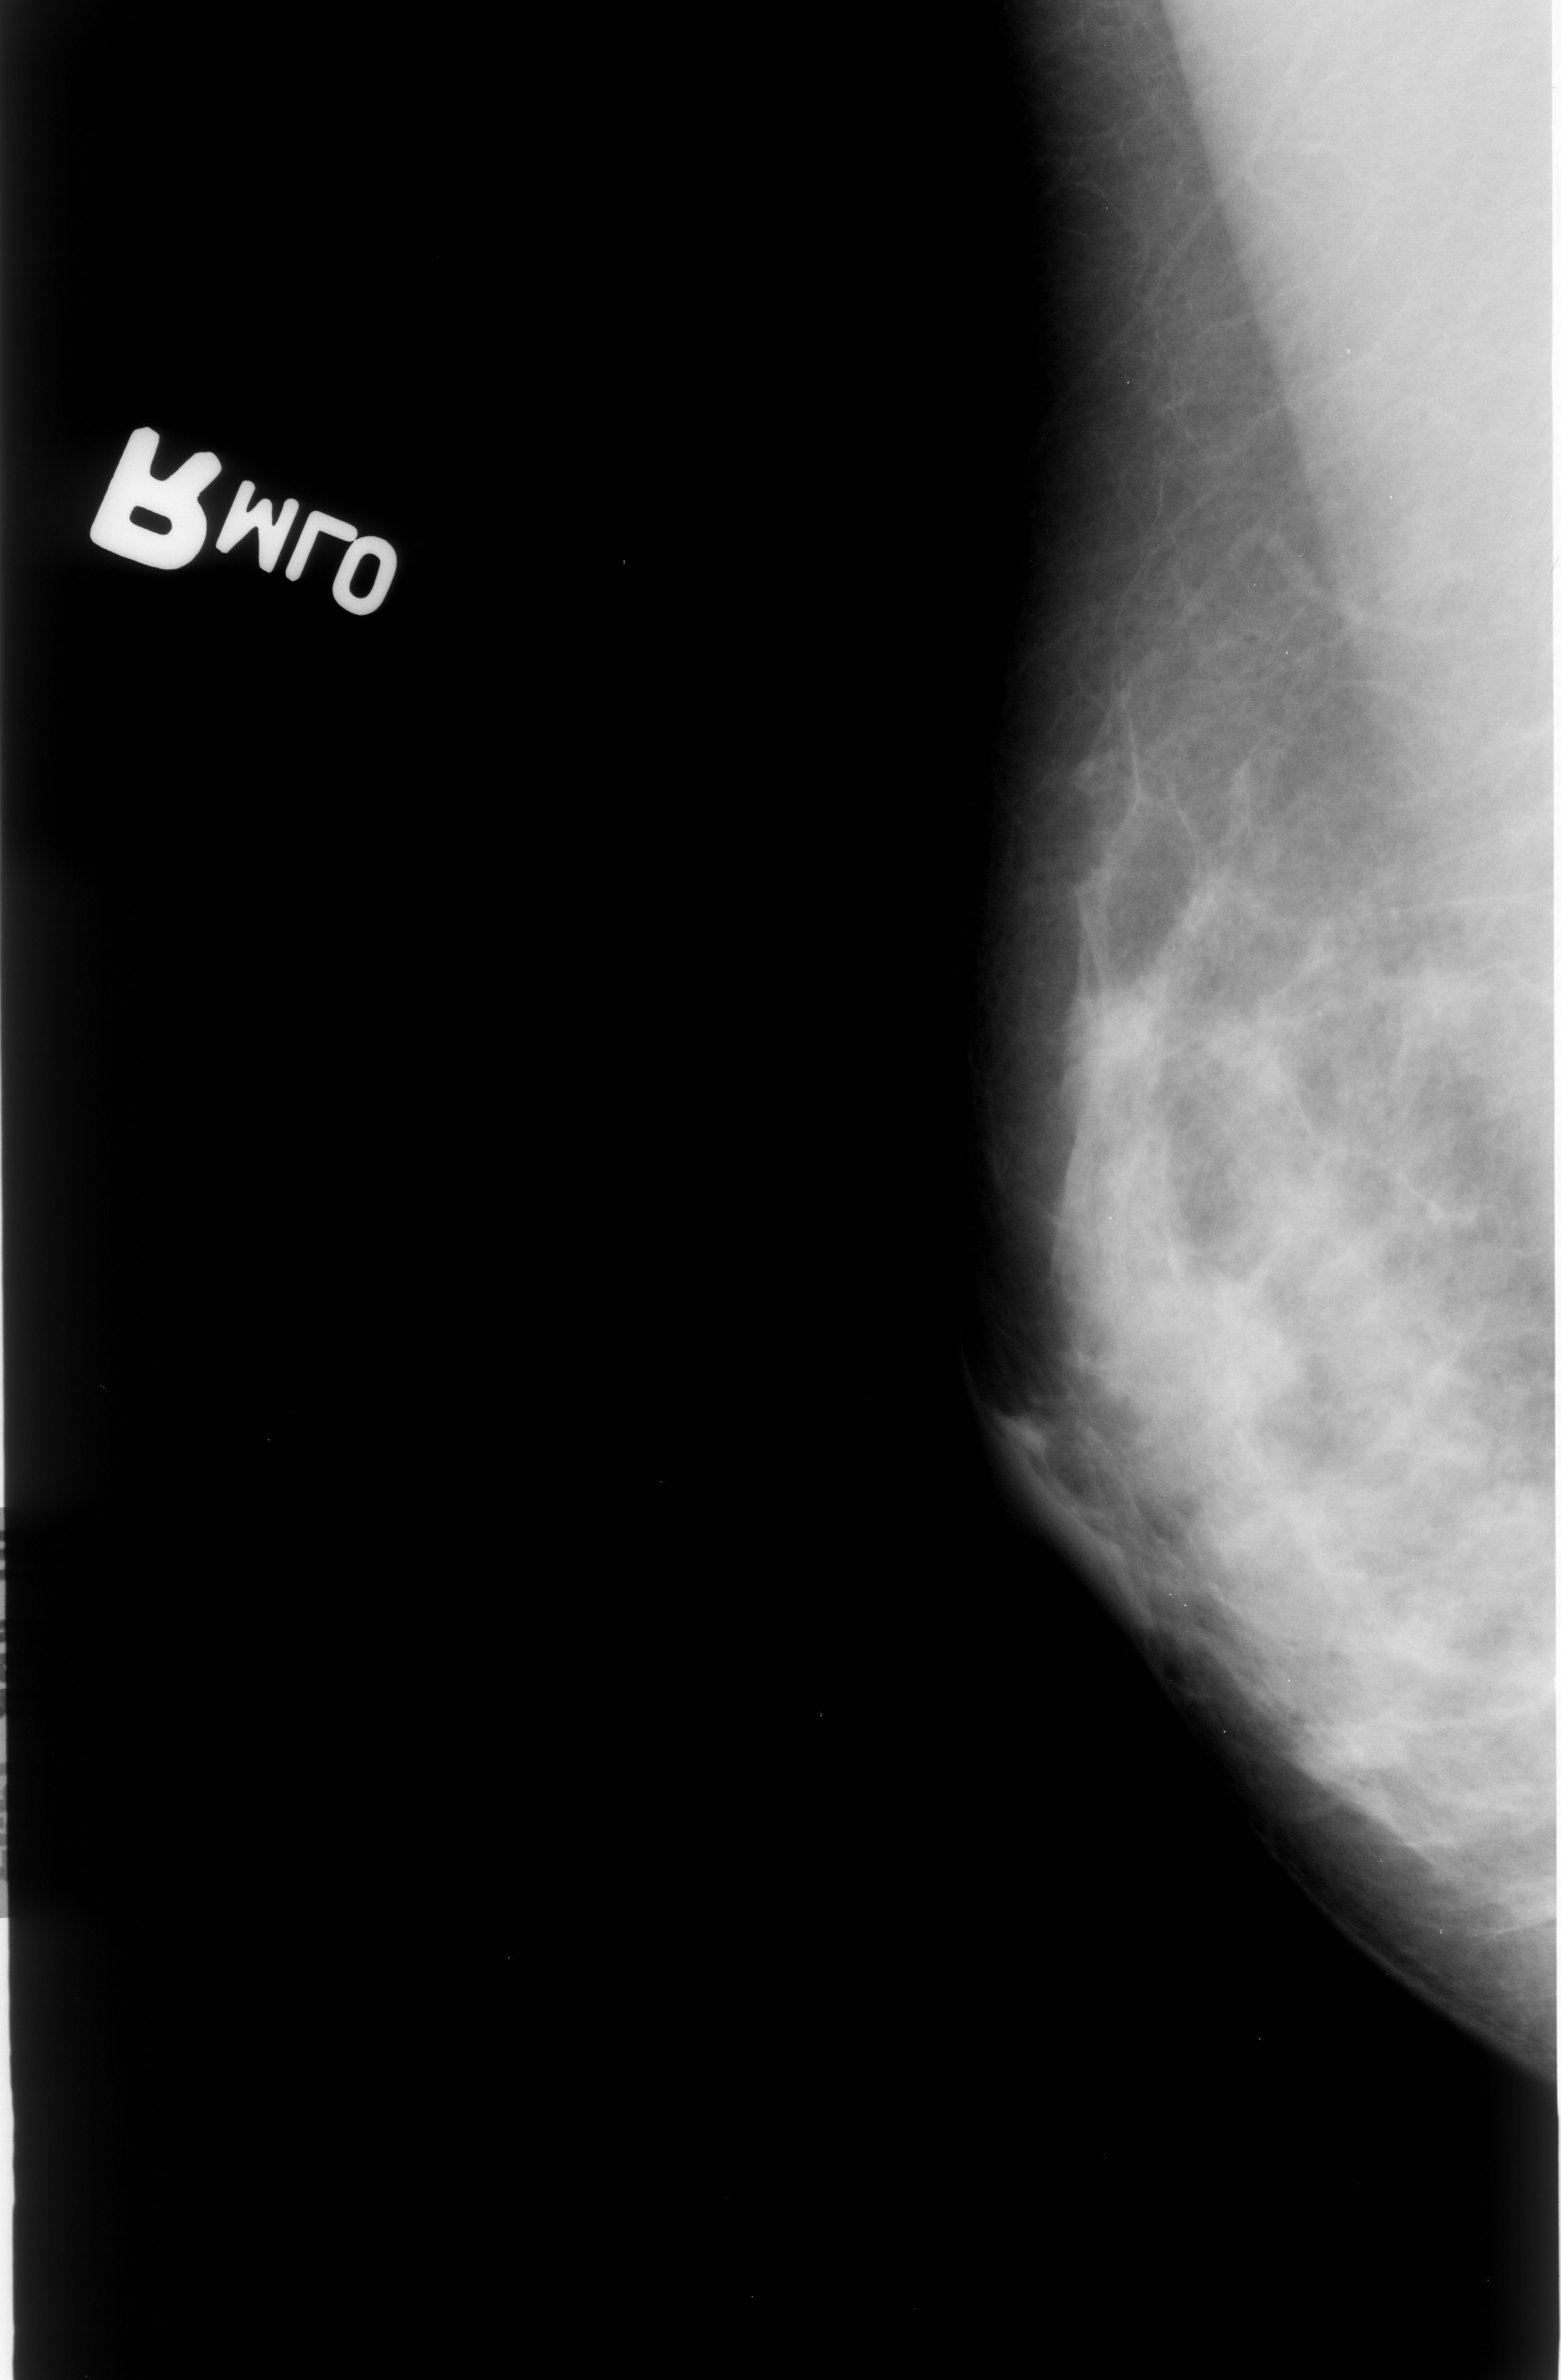
Digitized screen-film mammogram; right breast; MLO view; 1561 × 2380 image matrix.
Expert-marked regions of interest on this image (one box per marked abnormality):
- mass, shape irregular, margins obscured / ill defined; BI-RADS assessment category 3; pathology result (as recorded, not read from the image): malignant: bounding box [x1, y1, x2, y2] px = [1096, 1265, 1311, 1442]